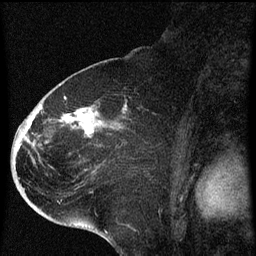
Breast MRI (dynamic contrast-enhanced), one sagittal slice; slice 34 of 60 in the series (ordered by position); dynamic contrast-enhanced series, image 2 of 4 at this slice position (ordered by acquisition); 1.5 T; TE 4.2 ms, TR 8 ms; 2 mm slice thickness; 256 × 256 image matrix, field of view 180 × 180 mm. Female patient, age 71 years.
Outlined on this slice (semi-automatic segmentation, software-assisted and operator-edited):
- analysis volume of interest (the breast-tissue region the enhancement analysis was run in; not a lesion): bounding box [x1, y1, x2, y2] px = [32, 86, 139, 205]
- tumour enhancement mask (voxels above the 70 % enhancement threshold inside the analysis volume of interest): [40, 96, 94, 137]